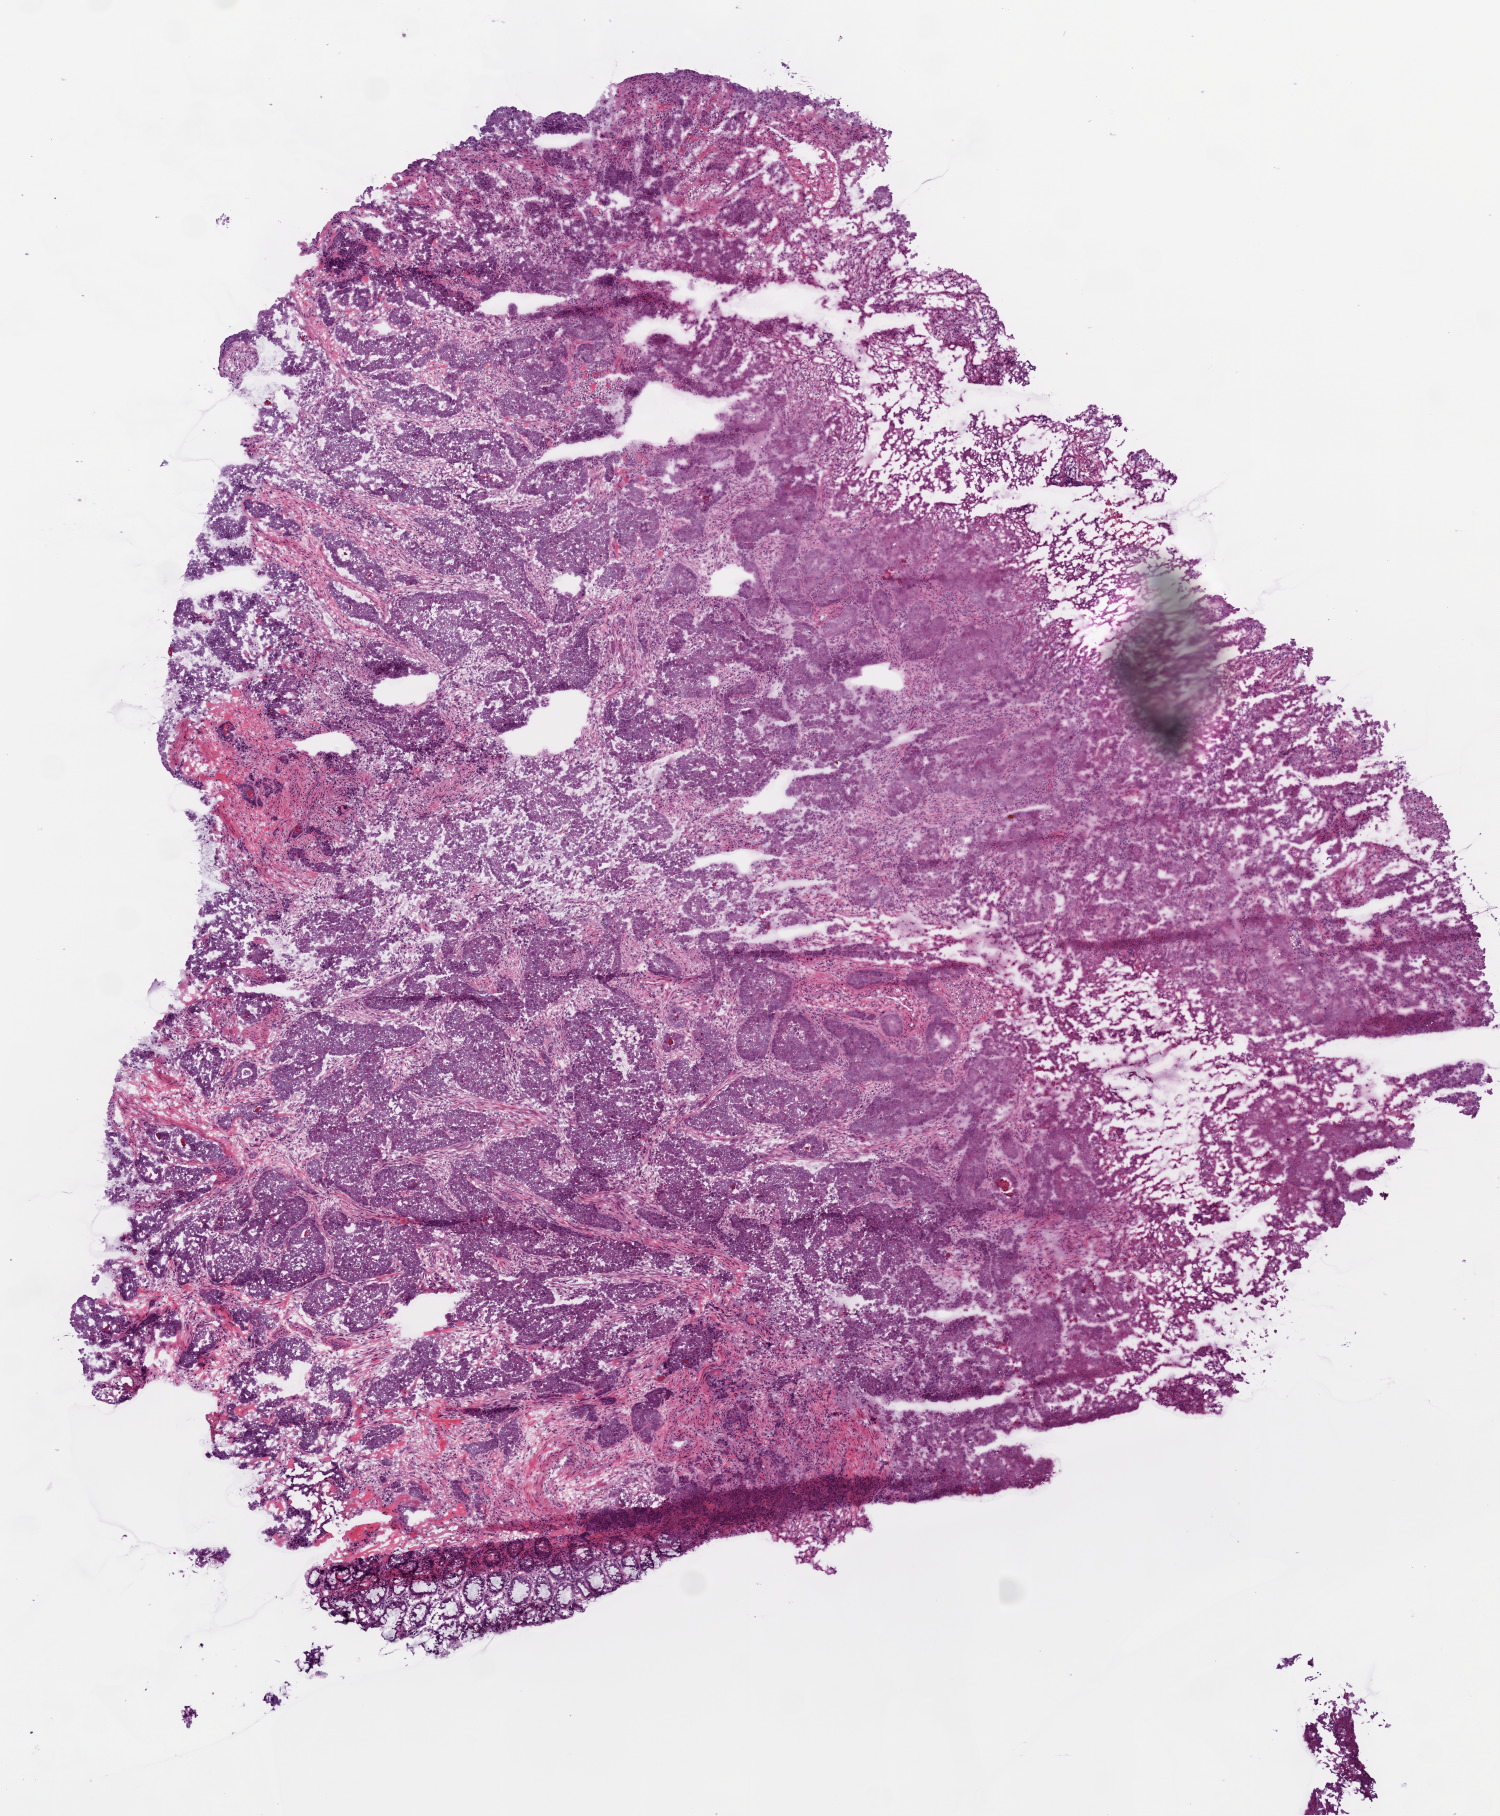
Digitized H&E-stained tissue section (whole slide), shown as a low-resolution overview of the whole scanned area (about 6.0 x 7.3 mm, from a 20x scan), frozen section from the bottom of the tissue portion, sample: primary tumour, colon. Patient: male, age at initial diagnosis 68 years. Pathologist review of this section (percent, as recorded): tumour cells 80%, tumour nuclei 90%, normal cells 1%, stromal cells 16%, necrosis 3%.
AJCC pathologic stage: IIIC (6th edition). Diagnosis: Adenocarcinoma, NOS (descending colon).